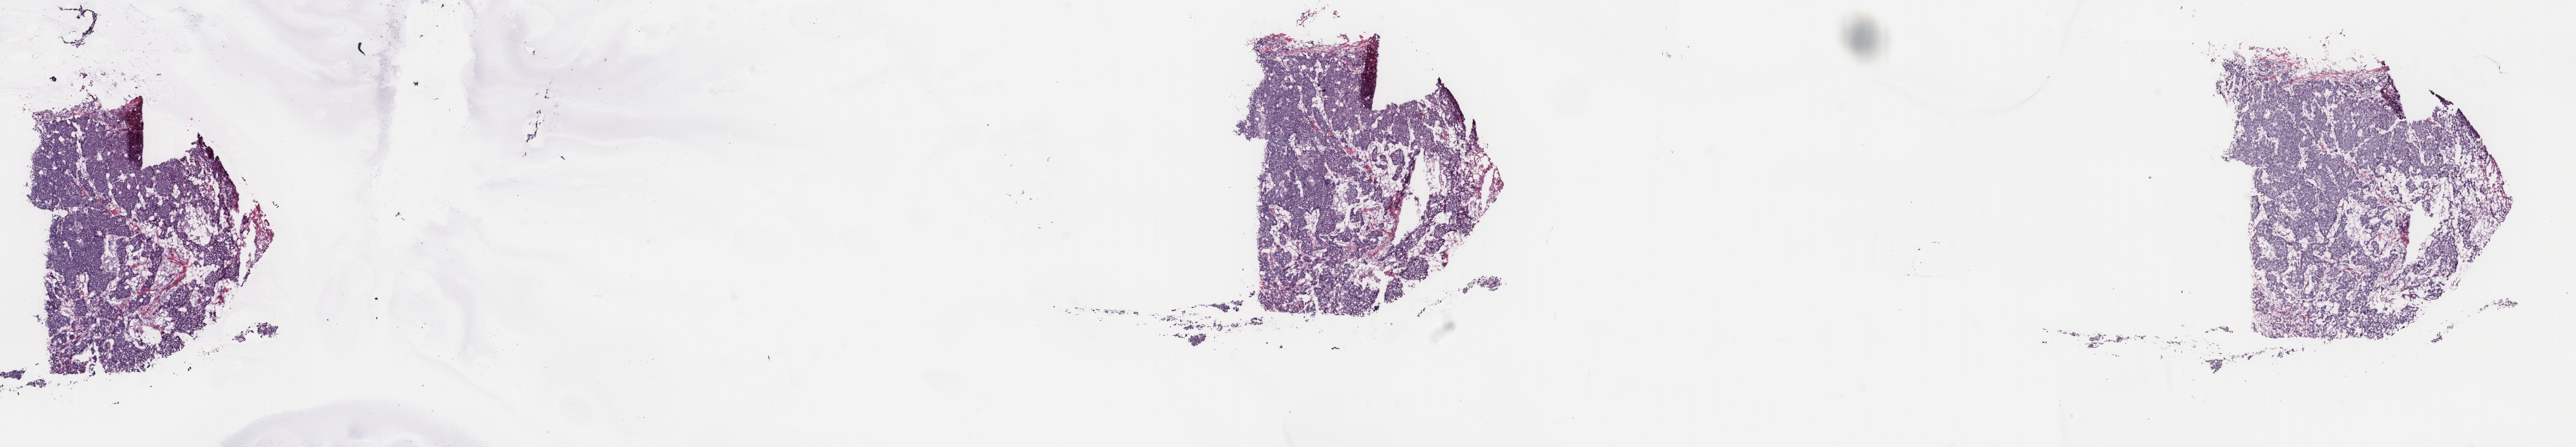
Whole-slide histology image, H&E-stained, whole scanned area (about 31.6 x 5.5 mm) shown as a low-resolution overview. Frozen section from the top of the tissue portion. Primary tumour sample from the breast. Female, age 57 years at initial diagnosis. Composition of this section per pathologist review: tumour cells 70%, tumour nuclei 90%, normal cells 0%, stromal cells 25%, necrosis 5%. Infiltration values recorded for this section: lymphocyte infiltration 2%, monocyte infiltration 0%, neutrophil infiltration 0%.
Histologic diagnosis: Infiltrating duct carcinoma, NOS. AJCC pathologic stage: IIA (6th edition). Laterality: left.